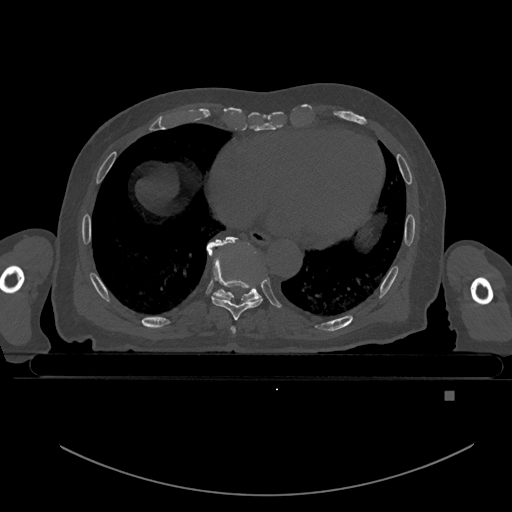
CT including the spine, one axial slice; position 184 of 969 along the scan axis; bone window (W 1800 / L 400 HU); 0.5 mm slice thickness; 512 × 512 image matrix, field of view 456 × 456 mm. Patient: male, 82 years. Case-level facts recorded for this patient, not image findings: primary cancer: prostate.
Outlined on this slice (semi-automatic segmentation, software-assisted and operator-edited):
- T7 vertebra: box from (x=231, y=326) to (x=236, y=334) px
- T8 vertebra: (x=212, y=241)–(x=263, y=320)
- T9 vertebra: (x=206, y=236)–(x=261, y=302)